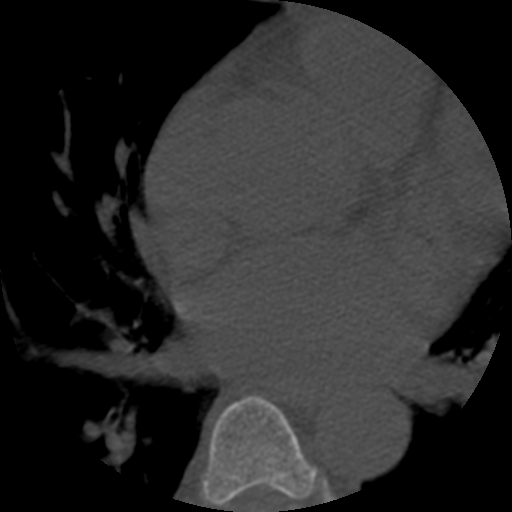
CT including the spine, one axial slice; slice 350 of 508 in the series (ordered by position); 120 kVp; bone window (W 1800 / L 400 HU); 512 × 512 image matrix, field of view 160 × 160 mm. Patient age 57 years. From the clinical record (not read from this slice): primary cancer: prostate.
Structures marked on this image (semi-automatically segmented with operator editing):
- T6 vertebra: bounding box [x1, y1, x2, y2] px = [202, 395, 319, 509]